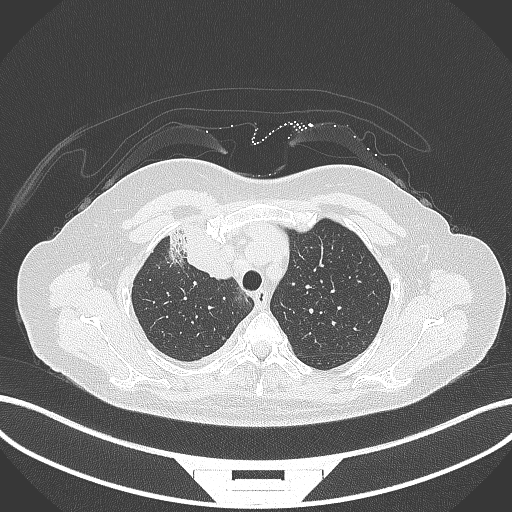
Chest CT, one axial slice; position 242 of 305 along the scan axis; reconstruction kernel B70f; lung window (W 1500 / L -600 HU); 512 × 512 image matrix, field of view 400 × 400 mm. Female patient, age 52 years. From the clinical record (not read from this slice): clinical TNM (as recorded): T3 N1 M1.
Annotated regions visible in this slice (bounding box drawn by a radiologist):
- lung tumour (recorded histology: adenocarcinoma): box from (x=168, y=221) to (x=237, y=285) px